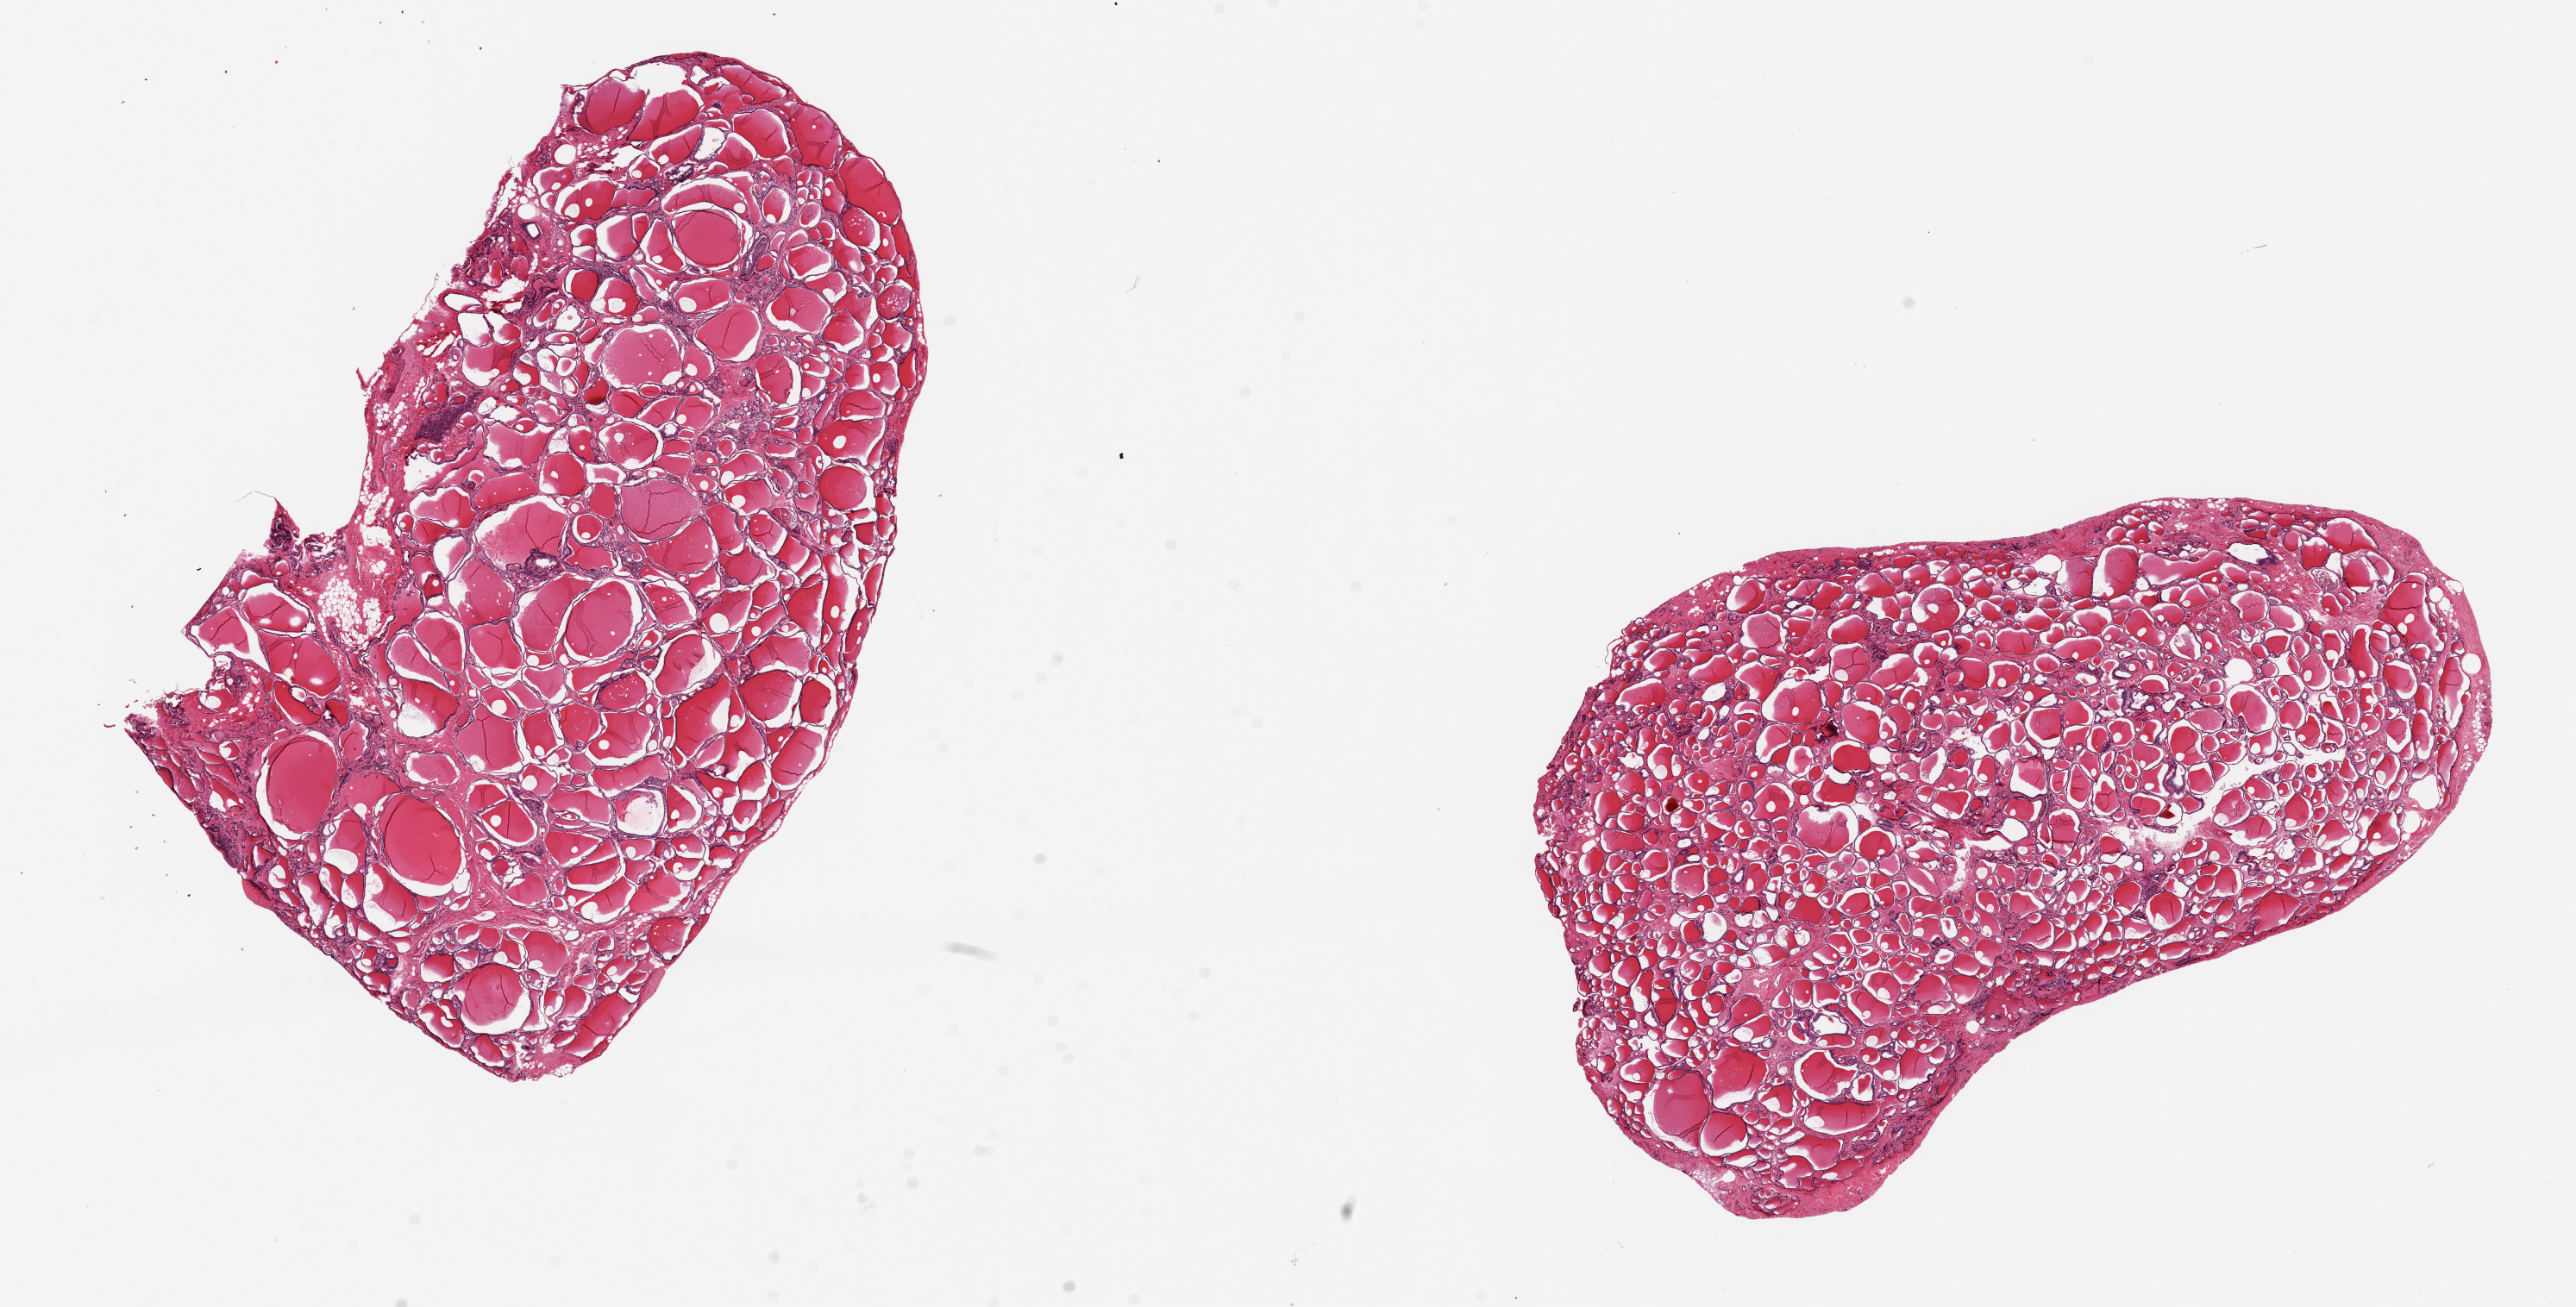
Digitized hematoxylin and eosin (H&E)-stained section, brightfield, whole scanned area (about 23.6 x 12.0 mm) shown as a low-resolution overview. PAXgene-fixed paraffin-embedded (PFPE) section. Section of thyroid (target tissue). Donor tissue sample. Female donor.
* pathologist's review note for this sample: 2 pieces, 9x6 & 9x5.5mm